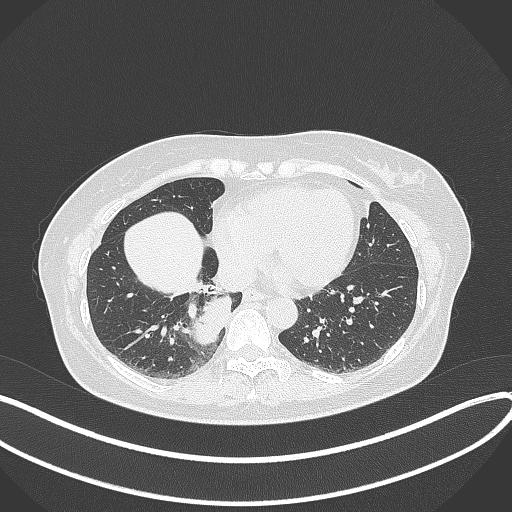
Chest CT, one axial slice. Position 113 of 331 along the scan axis. Reconstruction kernel B70f. 120 kVp. Lung window (W 1500 / L -600 HU). 512 × 512 image matrix, field of view 400 × 400 mm. Patient: female, 54 years. From the clinical record (not read from this slice): clinical TNM (as recorded): T4 N0 M0.
Structures marked on this image (bounding box drawn by a radiologist):
- lung tumour (recorded histology: adenocarcinoma): bounding box <192,288,239,347> (left, top, right, bottom; pixels)